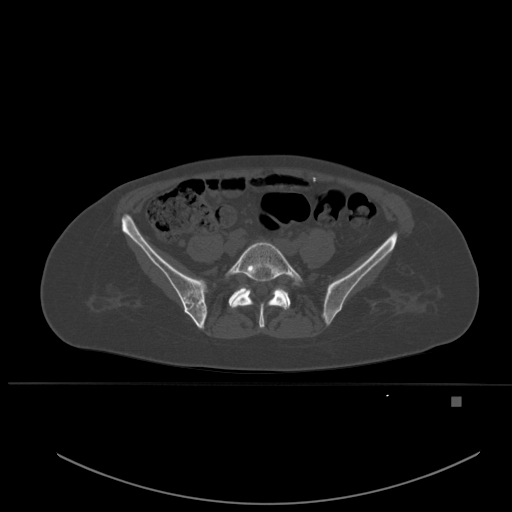
CT including the spine, one axial slice. Slice 151 of 651 in the series (ordered by position). Bone window (W 1800 / L 400 HU). 512 × 512 image matrix, field of view 443 × 443 mm. Patient: female, 49 years. From the clinical record (not read from this slice): primary cancer: breast; vertebrae with lytic lesions (as recorded): L3, T12, L4.
Outlined on this slice (semi-automatically segmented with operator editing):
- L5 vertebra: box from (x=226, y=242) to (x=302, y=328) px